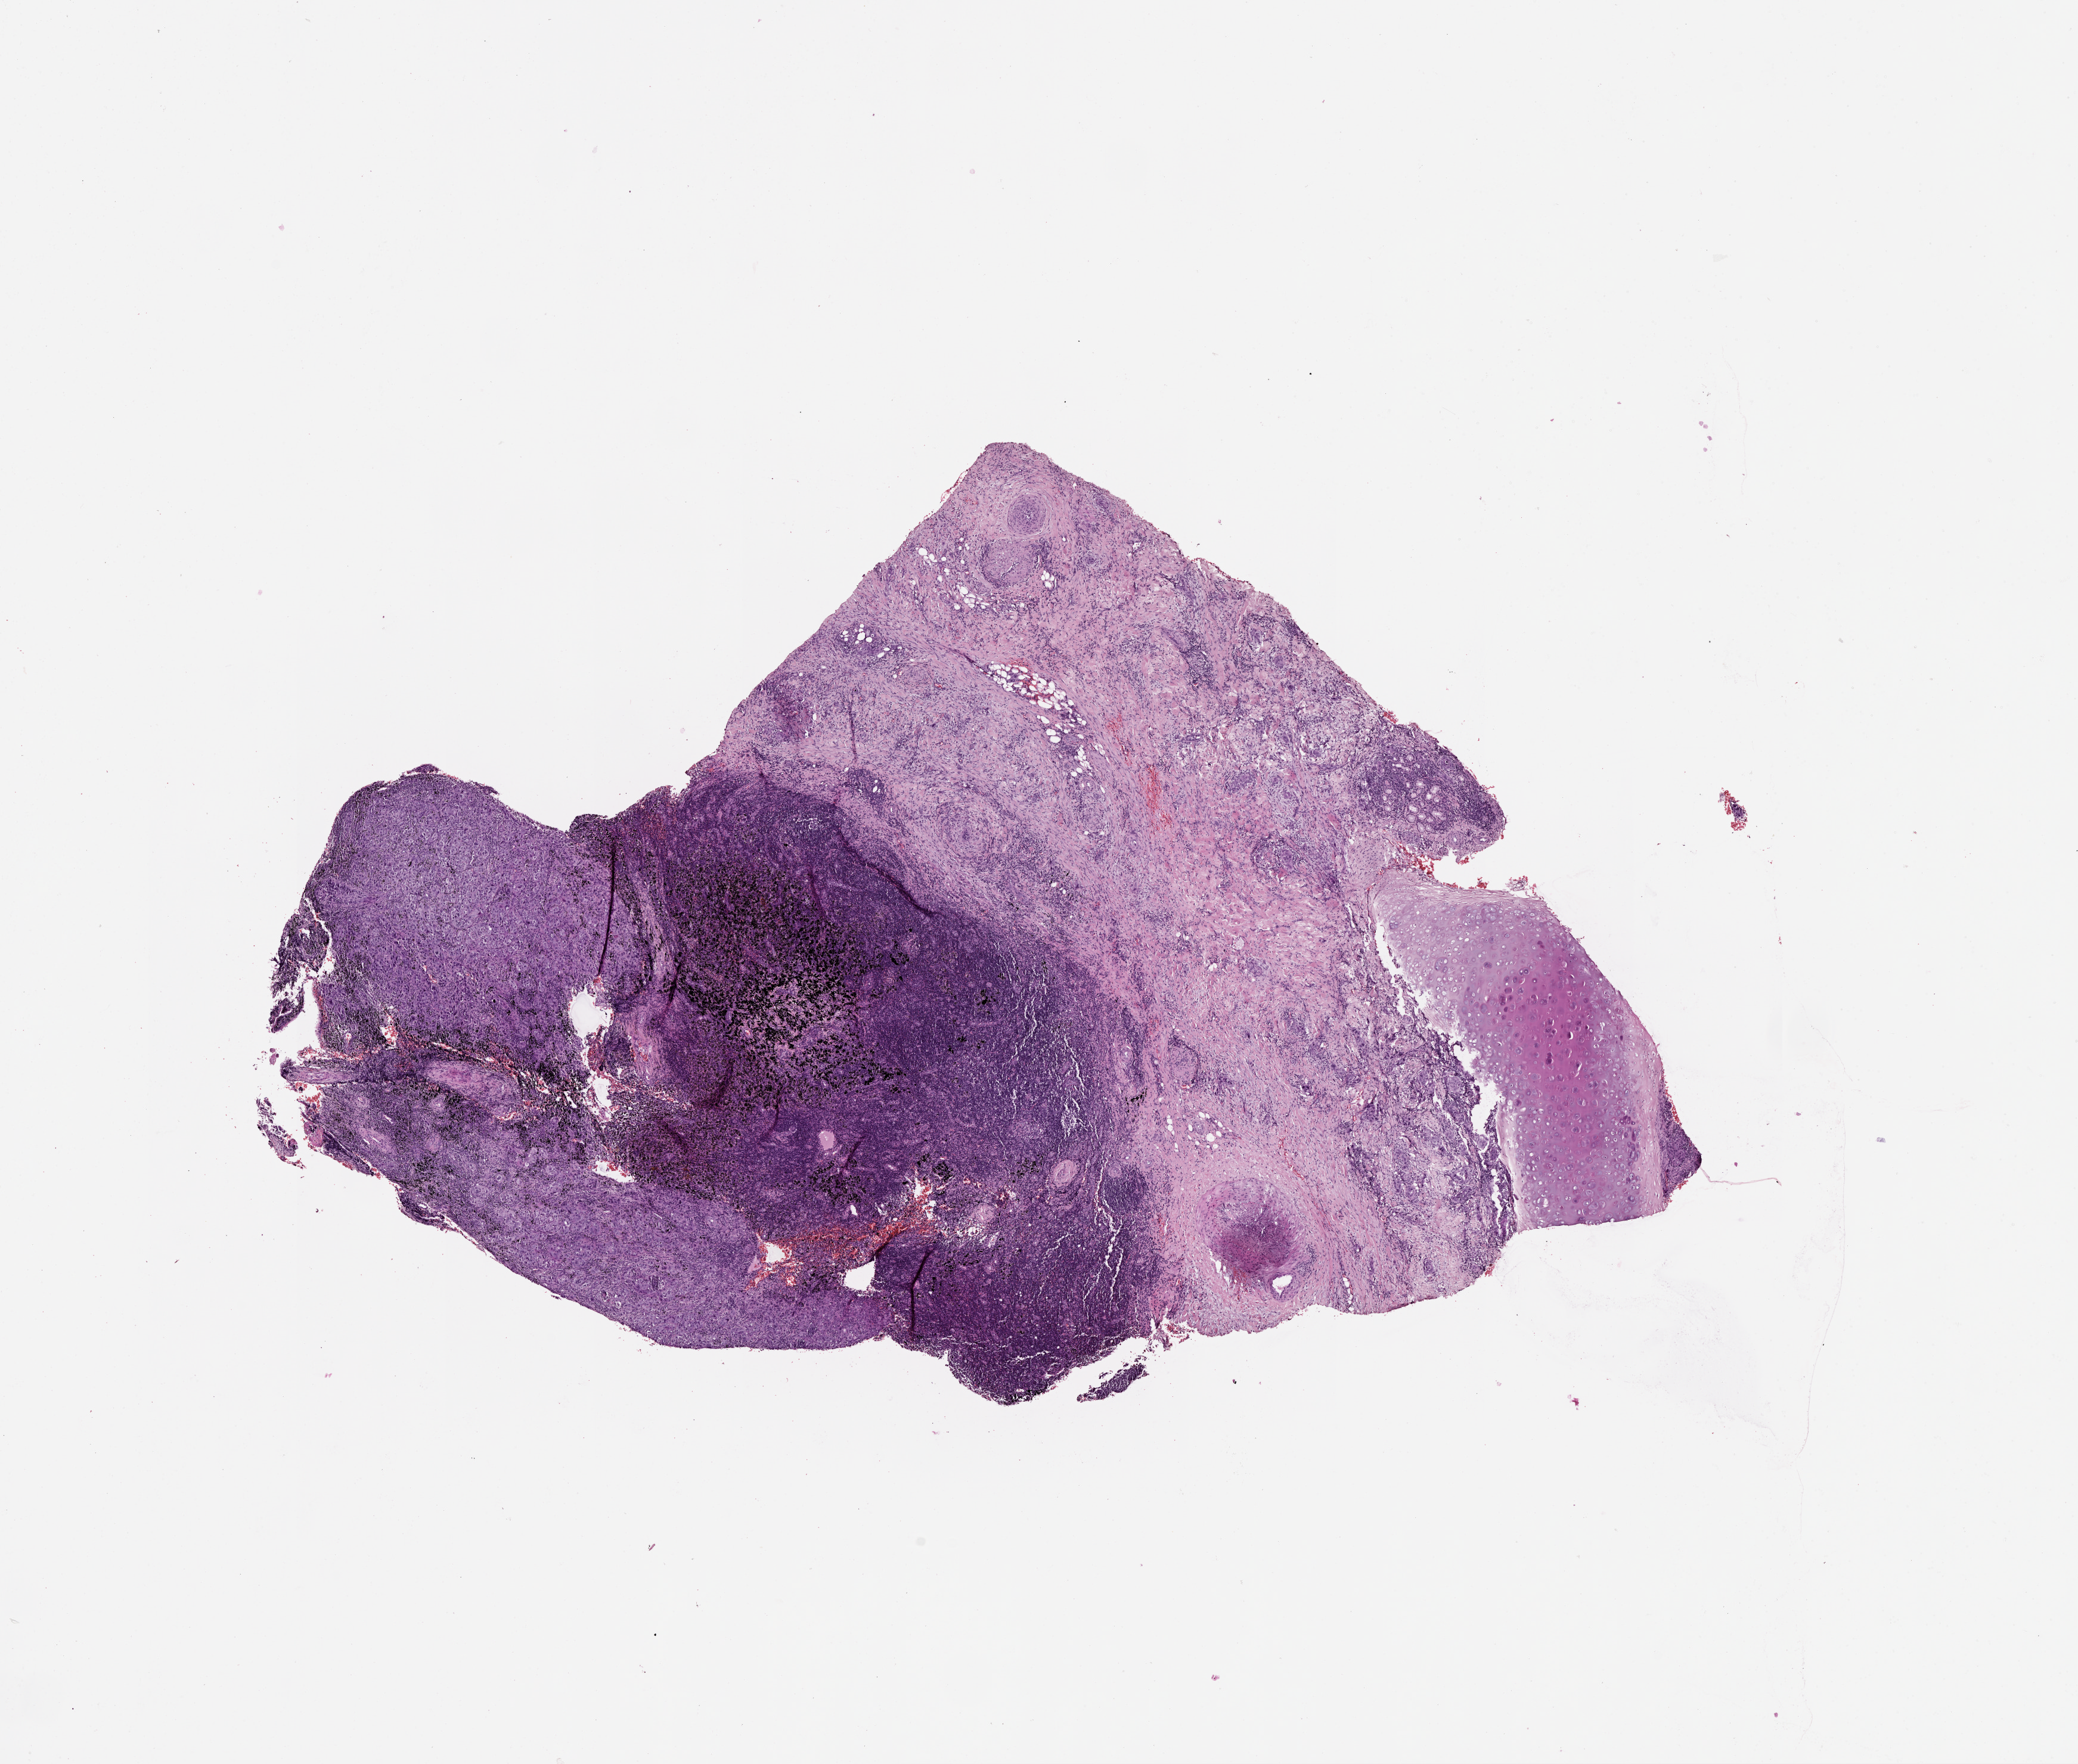
Whole-slide histology image, H&E-stained — low-resolution overview of the scanned area, about 14.0 x 11.9 mm (slide scanned at 20x), tumour tissue sample, lung. 56-year-old female patient.
• patient diagnosis (cohort enrolment): squamous cell carcinoma (lung)